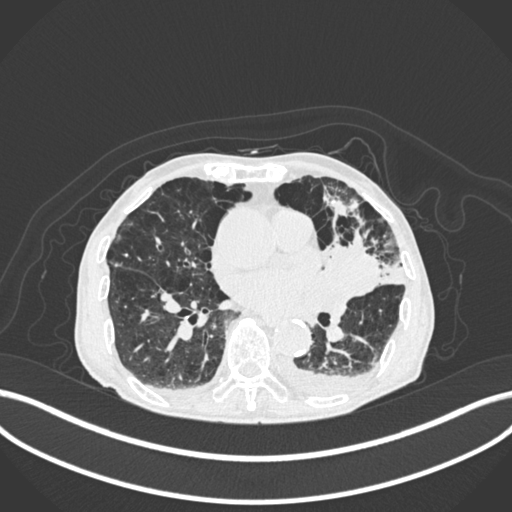
Chest CT, one axial slice; position 97 of 400 along the scan axis; reconstruction kernel B30f; lung window (W 1500 / L -600 HU); 512 × 512 image matrix, field of view 400 × 400 mm. Male patient, age 90 years or older. From the clinical record (not read from this slice): clinical TNM (as recorded): T2b N1 M0.
Structures marked on this image (rectangle marked by the reading radiologist):
- lung tumour (recorded histology: squamous cell carcinoma): bounding box (x1, y1, x2, y2) in pixels: (323, 235, 382, 296)